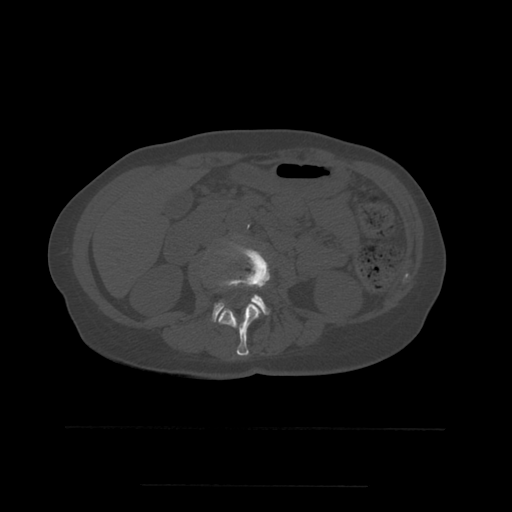
CT including the spine, one axial slice. Position 201 of 544 along the scan axis. Bone window (W 1800 / L 400 HU). 1.25 mm slice thickness. 512 × 512 image matrix. Patient age 58 years. Case-level facts recorded for this patient, not image findings: primary cancer: lung.
Annotated regions visible in this slice (semi-automatic segmentation, software-assisted and operator-edited):
- L2 vertebra: bounding box [x1, y1, x2, y2] px = [216, 244, 270, 356]
- L3 vertebra: [212, 287, 270, 322]